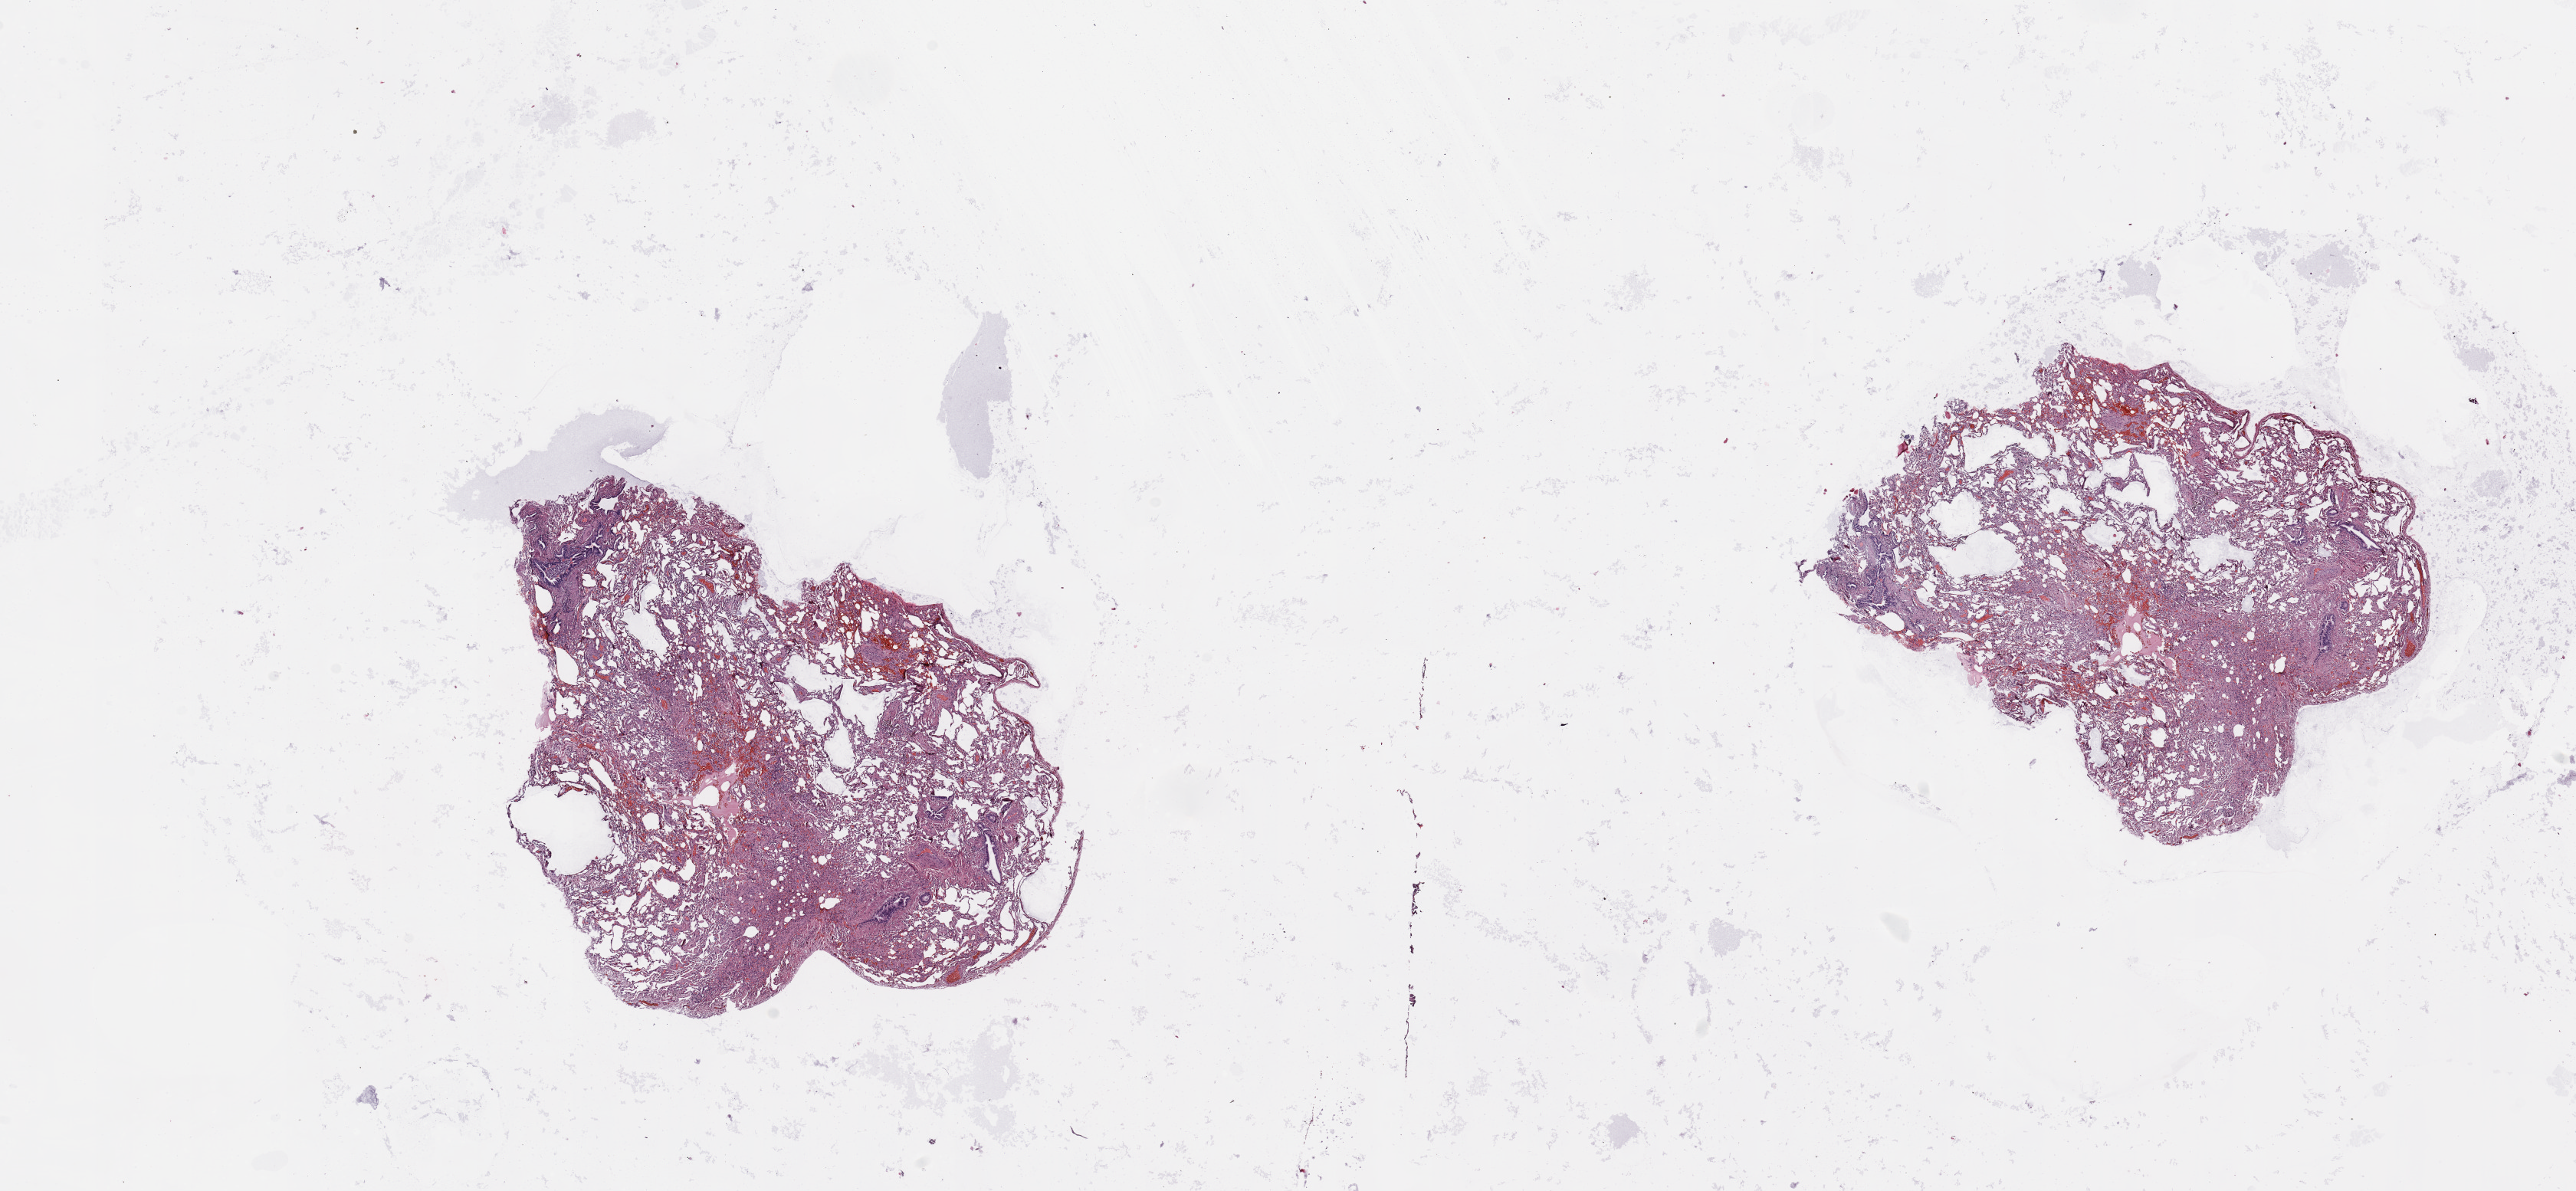
Whole-slide histology image, Hematoxylin and eosin (H&E) stained — shown as a low-resolution overview of the whole scanned area (about 26.6 x 12.3 mm, slide scanned at 20x). Normal (non-tumour) tissue sample, lung. Patient: male, age 63 years.
This section: normal (non-tumour) tissue from the same patient. Patient diagnosis (cohort enrolment): squamous cell carcinoma (lung).